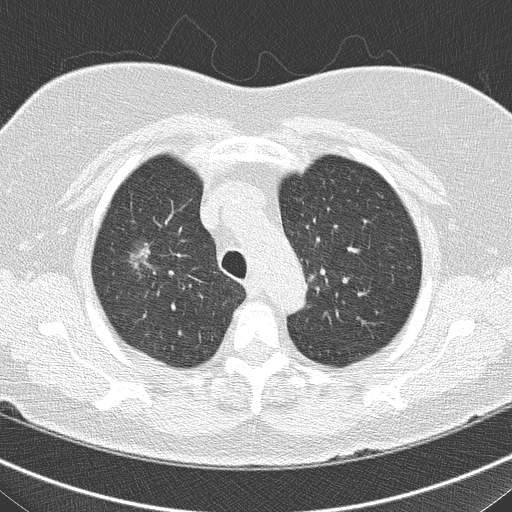
Low-dose screening chest CT, axial slice. Third annual screen. Lung window (W 1500 / L -600 HU). Female participant, aged 74 years at enrolment. Former smoker at enrolment.
- Expert-annotated lung lesion, bounding box (x1, y1, x2, y2) in pixels: (111, 233, 179, 296).
- The screening reader recorded 5 non-calcified nodules or masses ≥4 mm on this exam (right upper lobe, right middle lobe, right middle lobe, left lower lobe, right lower lobe); which of them this box marks is not recorded.
- Official screen result: positive, other.
- Later outcome: lung cancer diagnosed 117 days after this screen — bronchiolo-alveolar carcinoma, non-mucinous, right upper lobe, well differentiated (G1), stage IA (AJCC 6th edition), 14 mm at pathology.